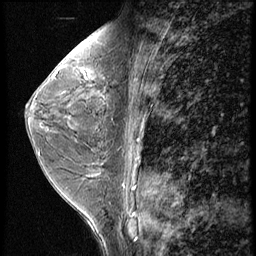
Breast MRI (dynamic contrast-enhanced), one sagittal slice. Slice 28 of 56 in the series (ordered by position). 3 images stored at this slice position (order not interpretable as contrast timing). 1.5 T. TE 4.2 ms, TR 9 ms. 2.5 mm slice thickness. 256 × 256 image matrix. Patient: female, 44 years. From the clinical record (not read from this slice): setting: breast cancer imaged before/during neoadjuvant chemotherapy; receptor status: triple-negative.
Annotated regions visible in this slice (semi-automatically segmented with operator editing):
- analysis volume of interest (the breast-tissue region the enhancement analysis was run in; not a lesion): bounding box (x1, y1, x2, y2) in pixels: (71, 54, 112, 99)
- tumour enhancement mask (voxels above the 140 % enhancement threshold inside the analysis volume of interest): (82, 71, 85, 74)